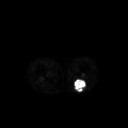
FDG PET of an extremity soft-tissue mass (from a PET/CT study), one axial slice; slice 196 of 267 in the series (ordered by position); 128 × 128 image matrix, field of view 500 × 500 mm. Patient: male, 54 years. Case-level facts recorded for this patient, not image findings: histological type: synovial sarcoma; site of the primary tumour: left poplietal fossa.
Annotated regions visible in this slice (expert contour drawn on MRI and transferred to this co-registered scan by the dataset authors):
- gross tumour volume (mass): bounding box [x1, y1, x2, y2] px = [73, 79, 87, 92]